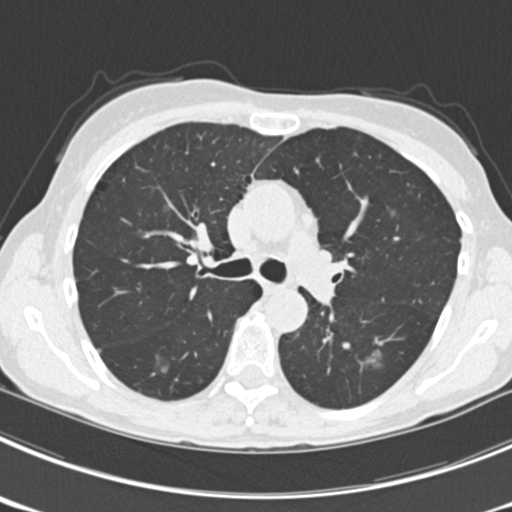
Axial slice from a low-dose chest CT screening exam. Third annual screen. Lung window (W 1500 / L -600 HU). 2 mm slice thickness. Standard (soft-tissue) reconstruction kernel (B30f). 512 × 512 image matrix. Female participant, aged 63 years at enrolment. Current smoker at enrolment.
2 expert reader's lesion annotations on this slice (largest first), box from (x=134, y=334) to (x=179, y=381) px; (x=357, y=343)–(x=397, y=381). The screening reader recorded 9 non-calcified nodules or masses ≥4 mm on this exam (left upper lobe, right upper lobe, left upper lobe, left lower lobe, right middle lobe, left lower lobe, left lower lobe, right lower lobe, right lower lobe); which of them these boxes mark is not recorded. Later outcome: lung cancer diagnosed 15 days after this screen — bronchiolo-alveolar adenocarcinoma, NOS, right upper lobe, right middle lobe, right lower lobe, left upper lobe, left lower lobe, moderately differentiated (G2), stage IV (AJCC 6th edition).